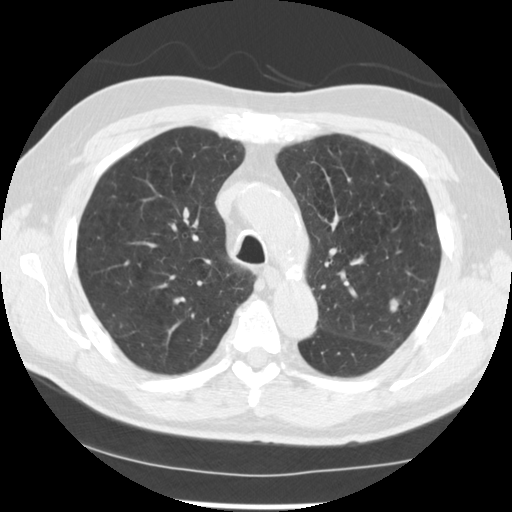
Axial slice from a low-dose chest CT screening exam. First (baseline) screen. Lung window (W 1500 / L -600 HU). 2.5 mm slice thickness. Slice 177 of 249 in the series. Male, age 71 years at enrolment. Current smoker at enrolment.
• Lesion marked by an expert reader, bounding box [x1, y1, x2, y2] px = [374, 283, 427, 333].
• The screening reader recorded 2 non-calcified nodules or masses ≥4 mm on this exam (left upper lobe, left upper lobe); which of them this box marks is not recorded.
• Later outcome: lung cancer diagnosed 37 days after this screen — adenocarcinoma, NOS, left upper lobe, poorly differentiated (G3), stage IIIB (AJCC 6th edition), 25 mm at pathology.